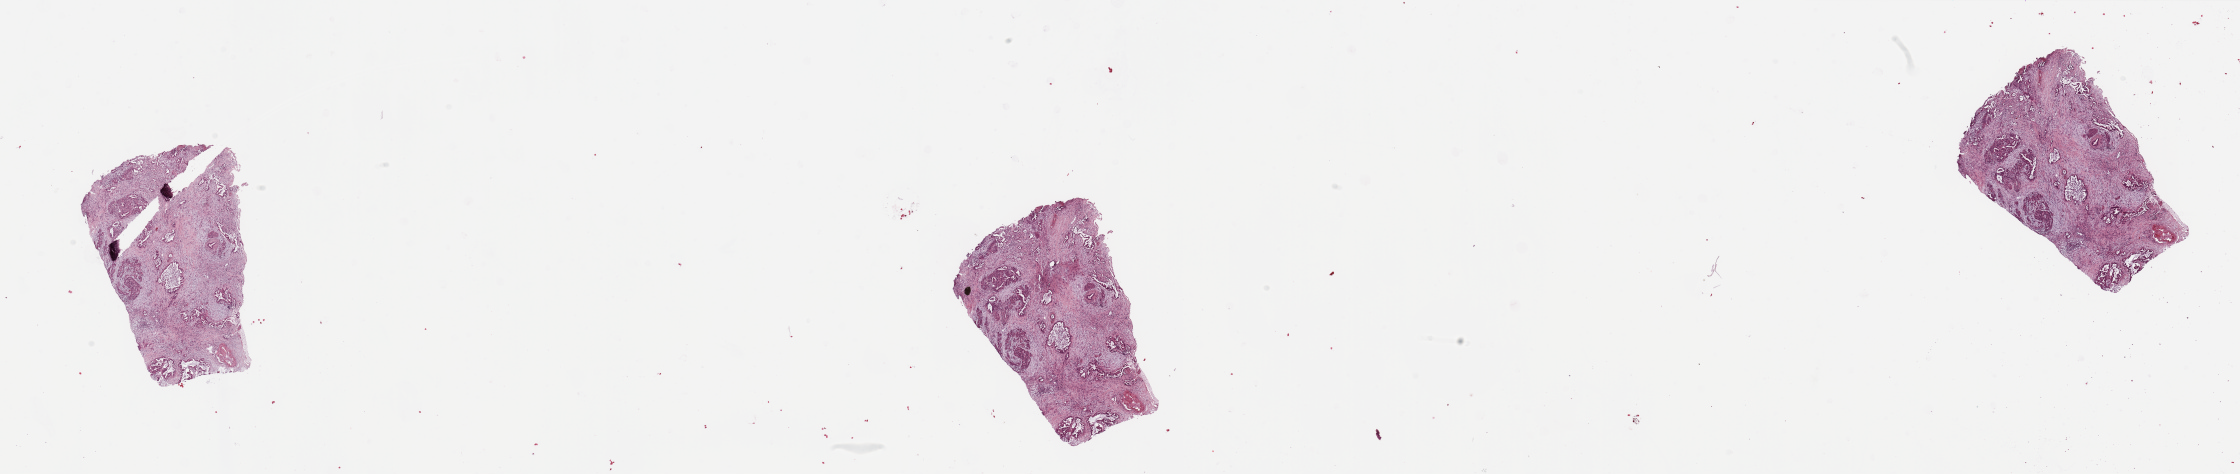
H&E whole-slide image — whole scanned area (about 35.4 x 7.5 mm) shown as a low-resolution overview, tumour tissue sample, sampled site: pancreas. Female, 70 y/o. Histologic grade: G2 (moderately differentiated). Composition of this section per pathologist review: tumour nuclei 30%, necrosis 2%.
Diagnosis: Infiltrating duct carcinoma, NOS. Primary tumour site (as recorded): head. AJCC pathologic stage: IIB.